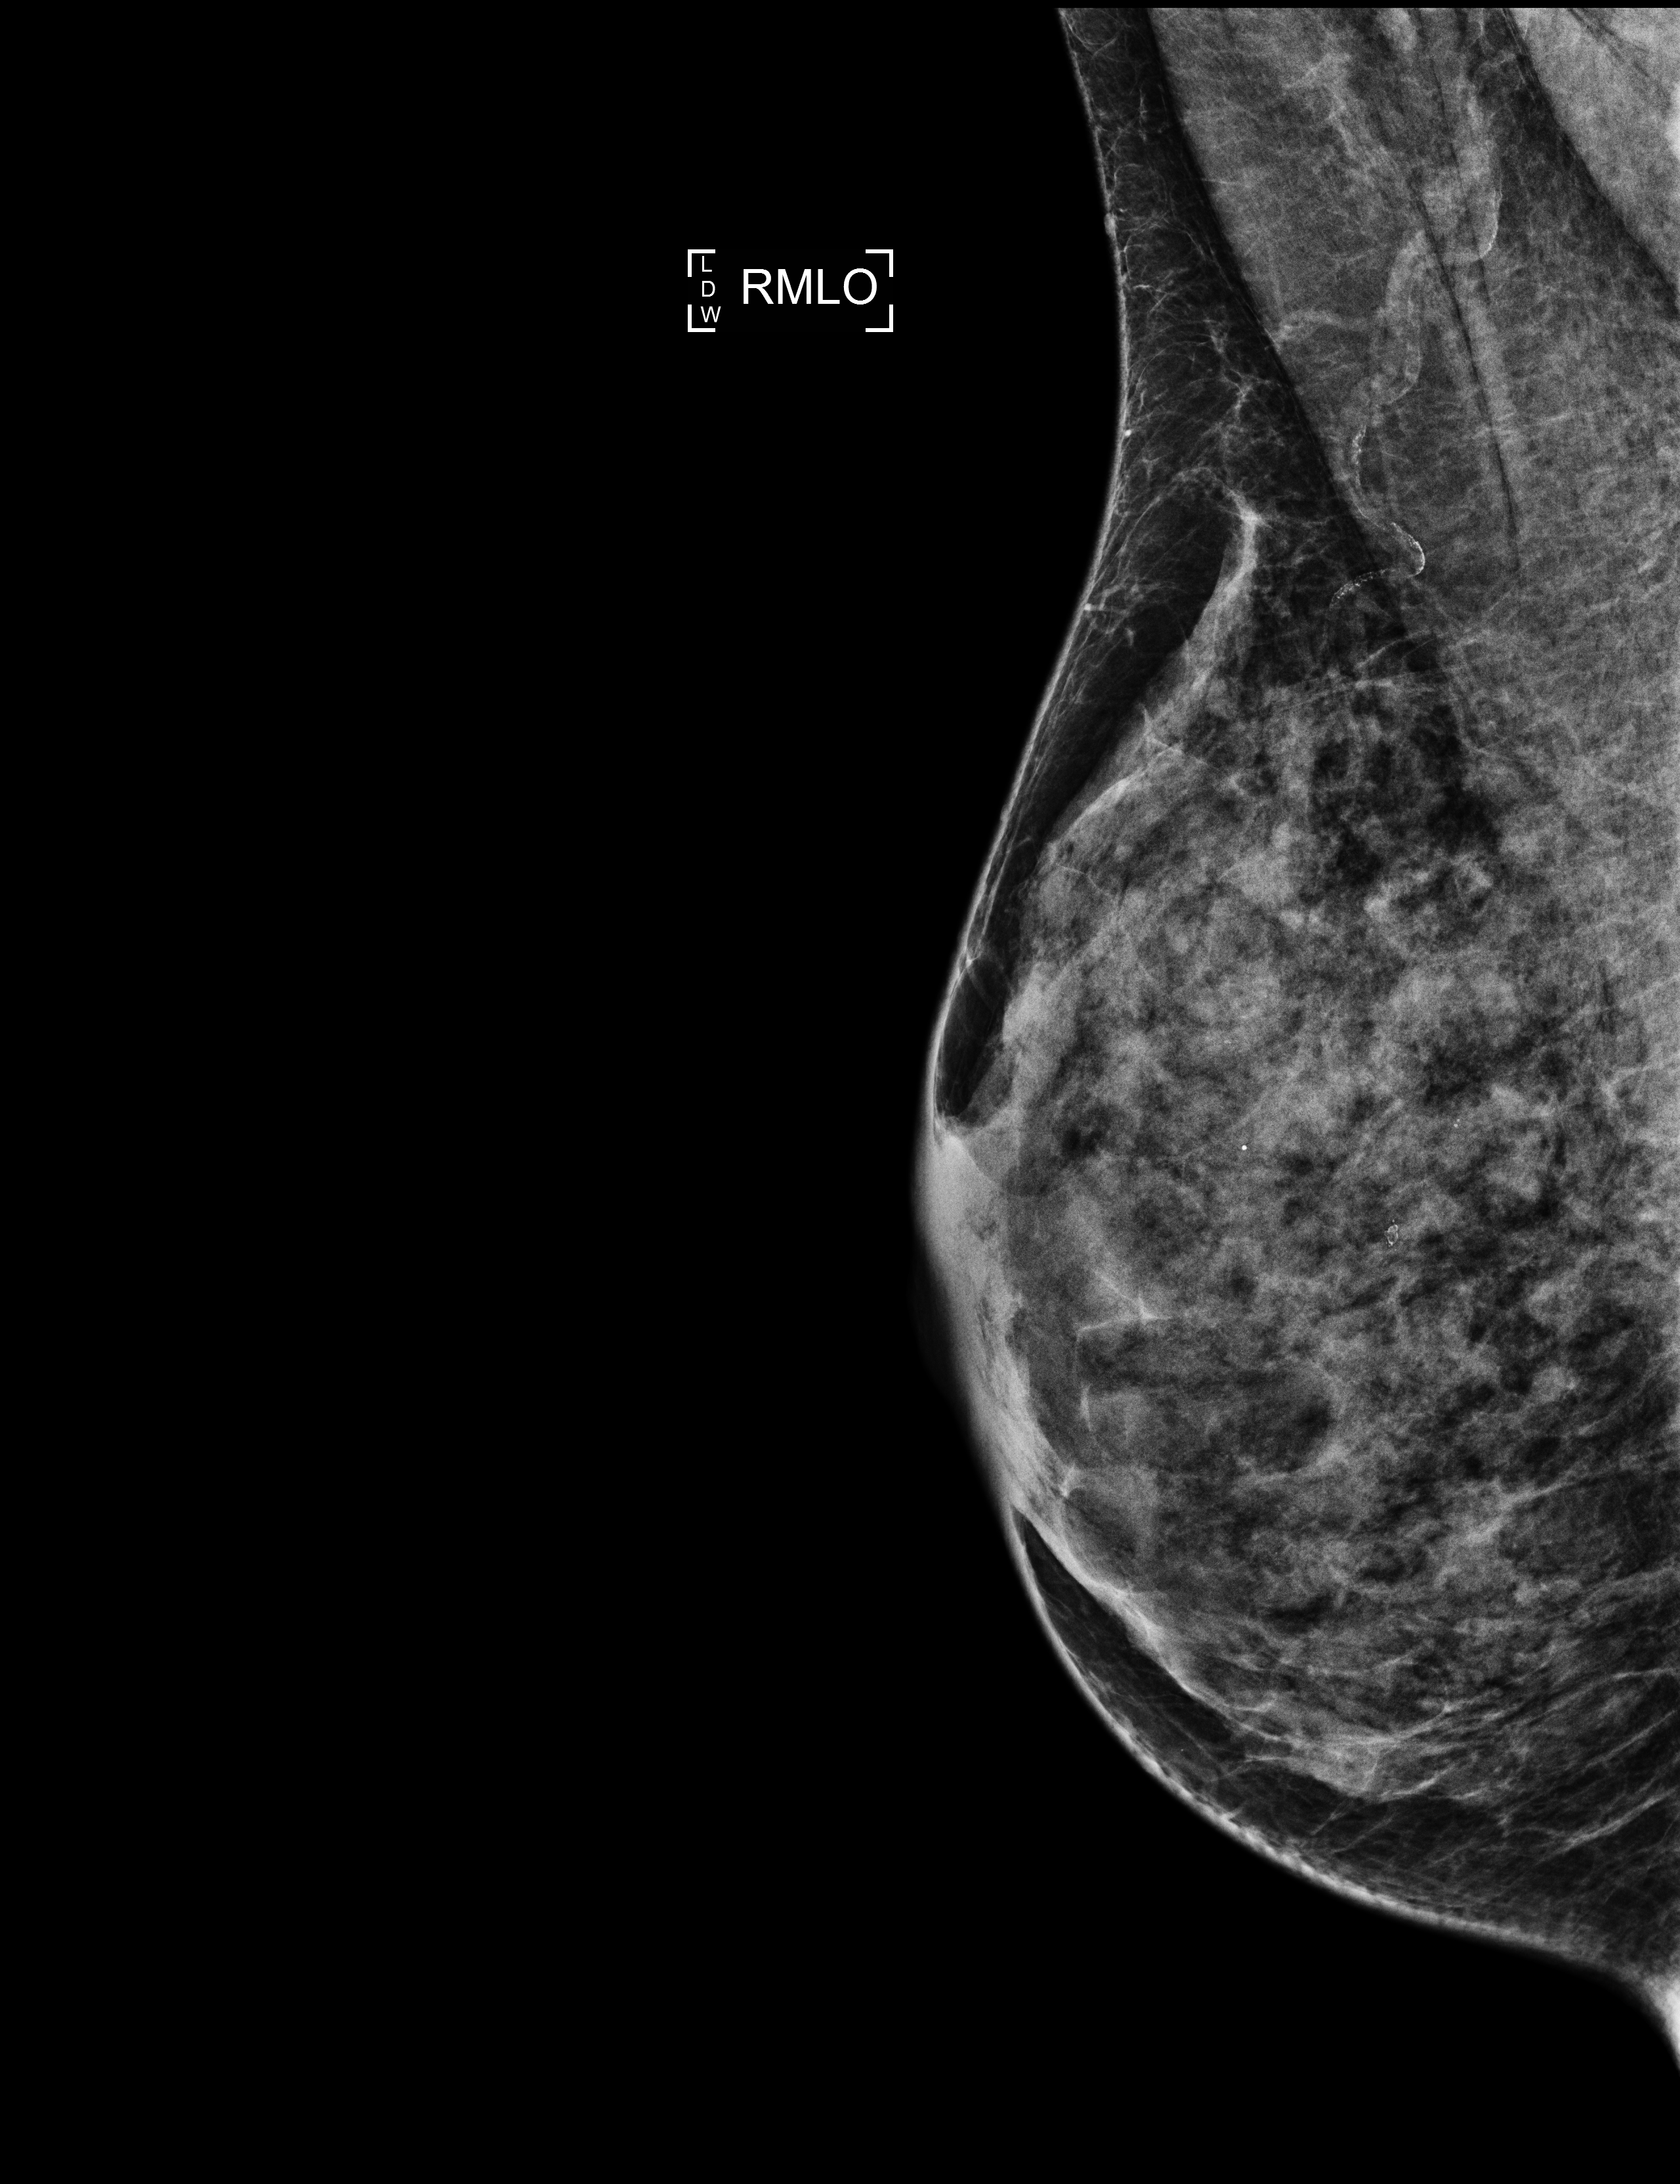
Screening examination, compressed breast thickness 38 mm, system: Selenia Dimensions. Patient: female, 57 years.
Image type: full-field digital mammogram. Breast: right. Projection: mediolateral oblique (MLO) view.